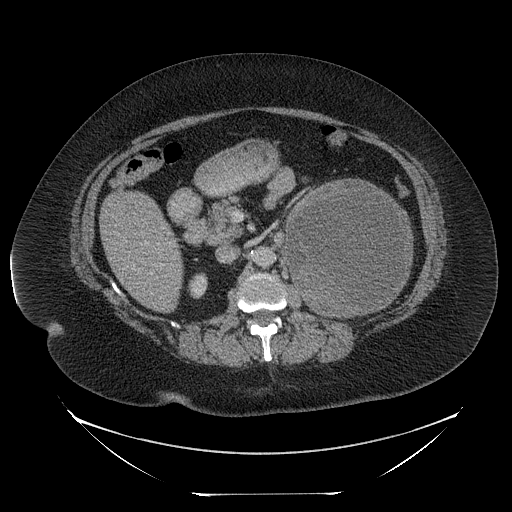
Contrast-enhanced abdominal CT, one axial slice; slice 131 of 205 in the series (ordered by position); reconstruction kernel STANDARD; 120 kVp; intravenous contrast given; soft-tissue window (W 400 / L 40 HU); 512 × 512 image matrix, field of view 500 × 500 mm. Female patient, age 53 years. Case-level facts recorded for this patient, not image findings: diagnosis: adrenocortical carcinoma; tumour side: left adrenal; tumour size at pathology: 17 cm; Ki-67 index: 20 %; stage (as recorded): 3.
Annotated regions visible in this slice (semi-automatic segmentation, software-assisted and operator-edited):
- mass: box from (x=287, y=181) to (x=412, y=317) px